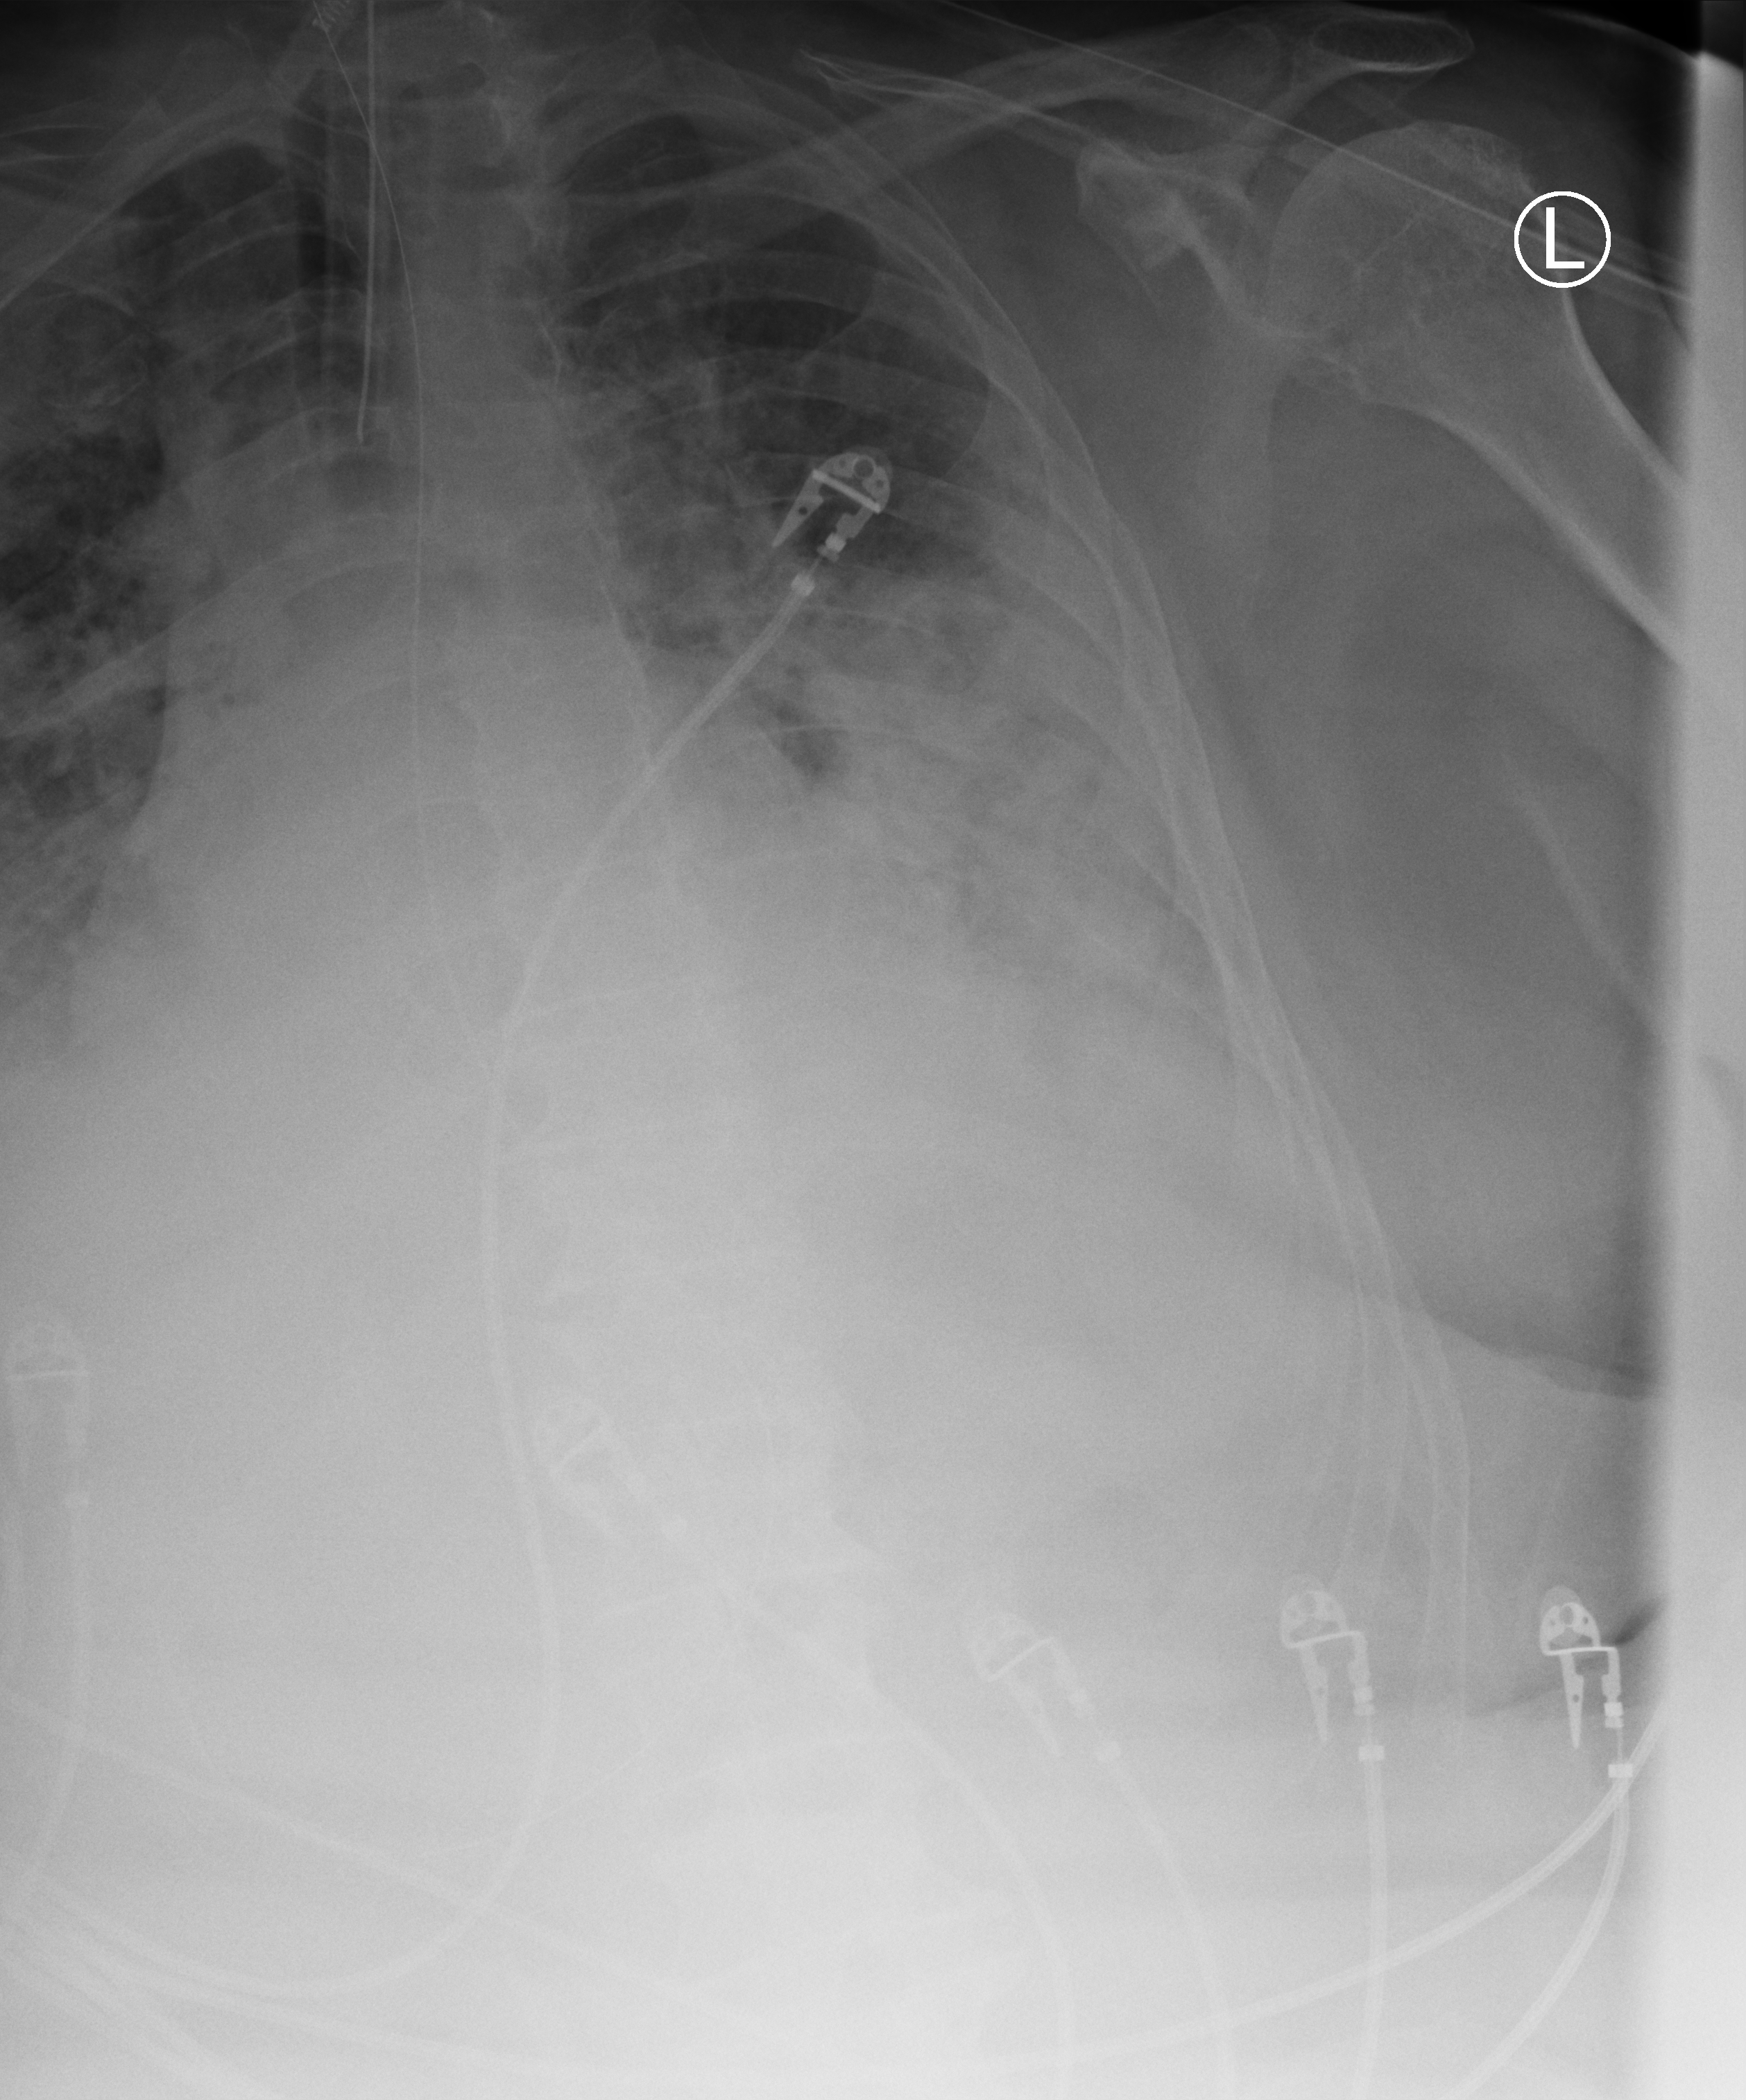
Portable chest radiograph; anteroposterior (AP) projection. Male patient hospitalised with COVID-19, age 60–74 years.
Admission-level facts for this patient (not findings on this image; timing relative to this image not recorded): length of hospital stay: 7 days; COPD (admission record): no; admitted to intensive care during this hospital stay: yes.